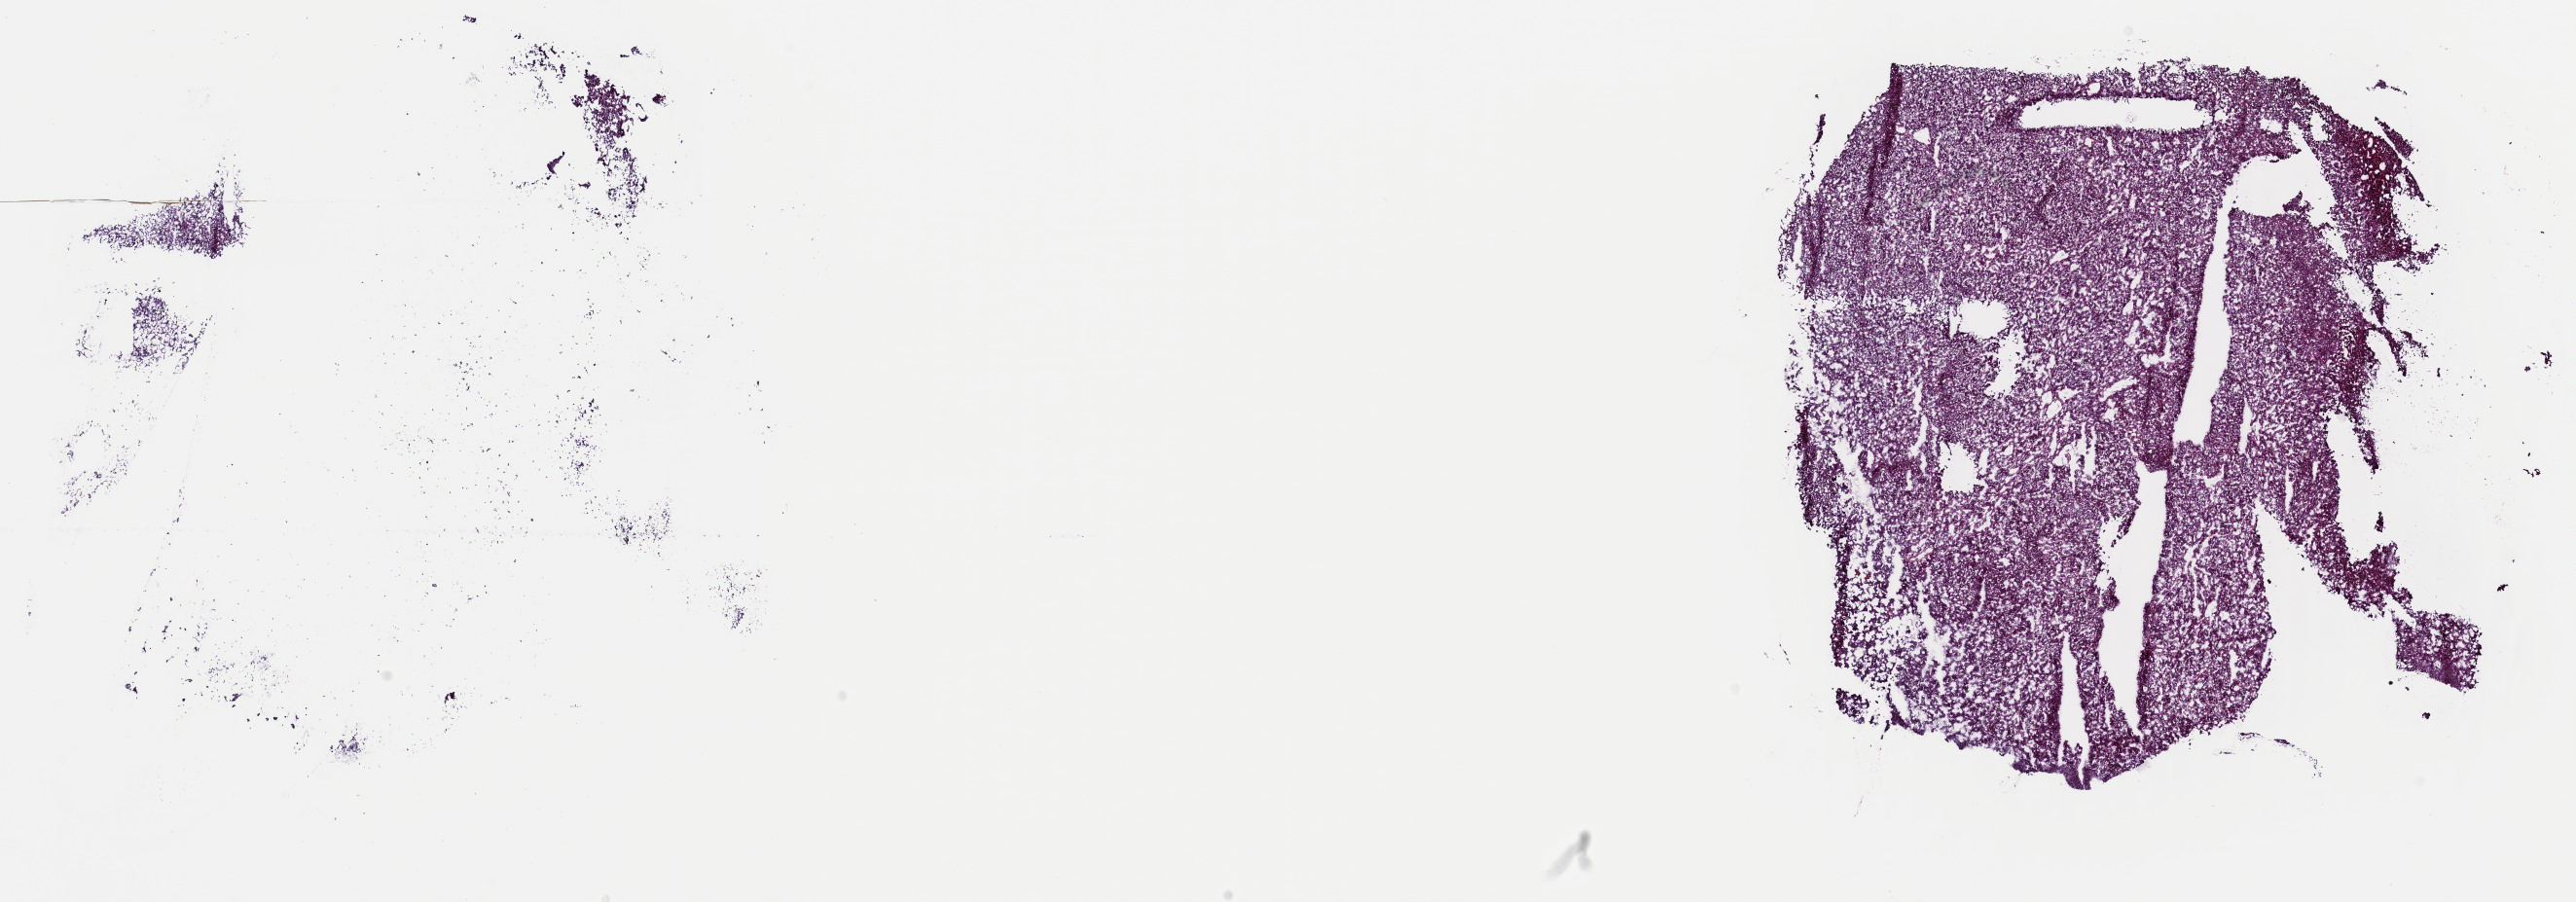
Whole-slide histology image, Hematoxylin and eosin (H&E) stained, a low-resolution overview of the entire scanned area, about 20.9 x 7.3 mm (acquisition: 40x scan). Frozen section. Sample: primary tumour, adrenal cortex. Female patient; age at initial diagnosis 20 years. Slide review estimates, as recorded: tumour cells 95%, tumour nuclei 100%, normal cells 0%, stromal cells 5%, necrosis 0%. Infiltration values recorded for this section: lymphocyte infiltration 0%, monocyte infiltration 0%, neutrophil infiltration 0%.
Histologic diagnosis: Adrenal cortical carcinoma (cortex of adrenal gland).